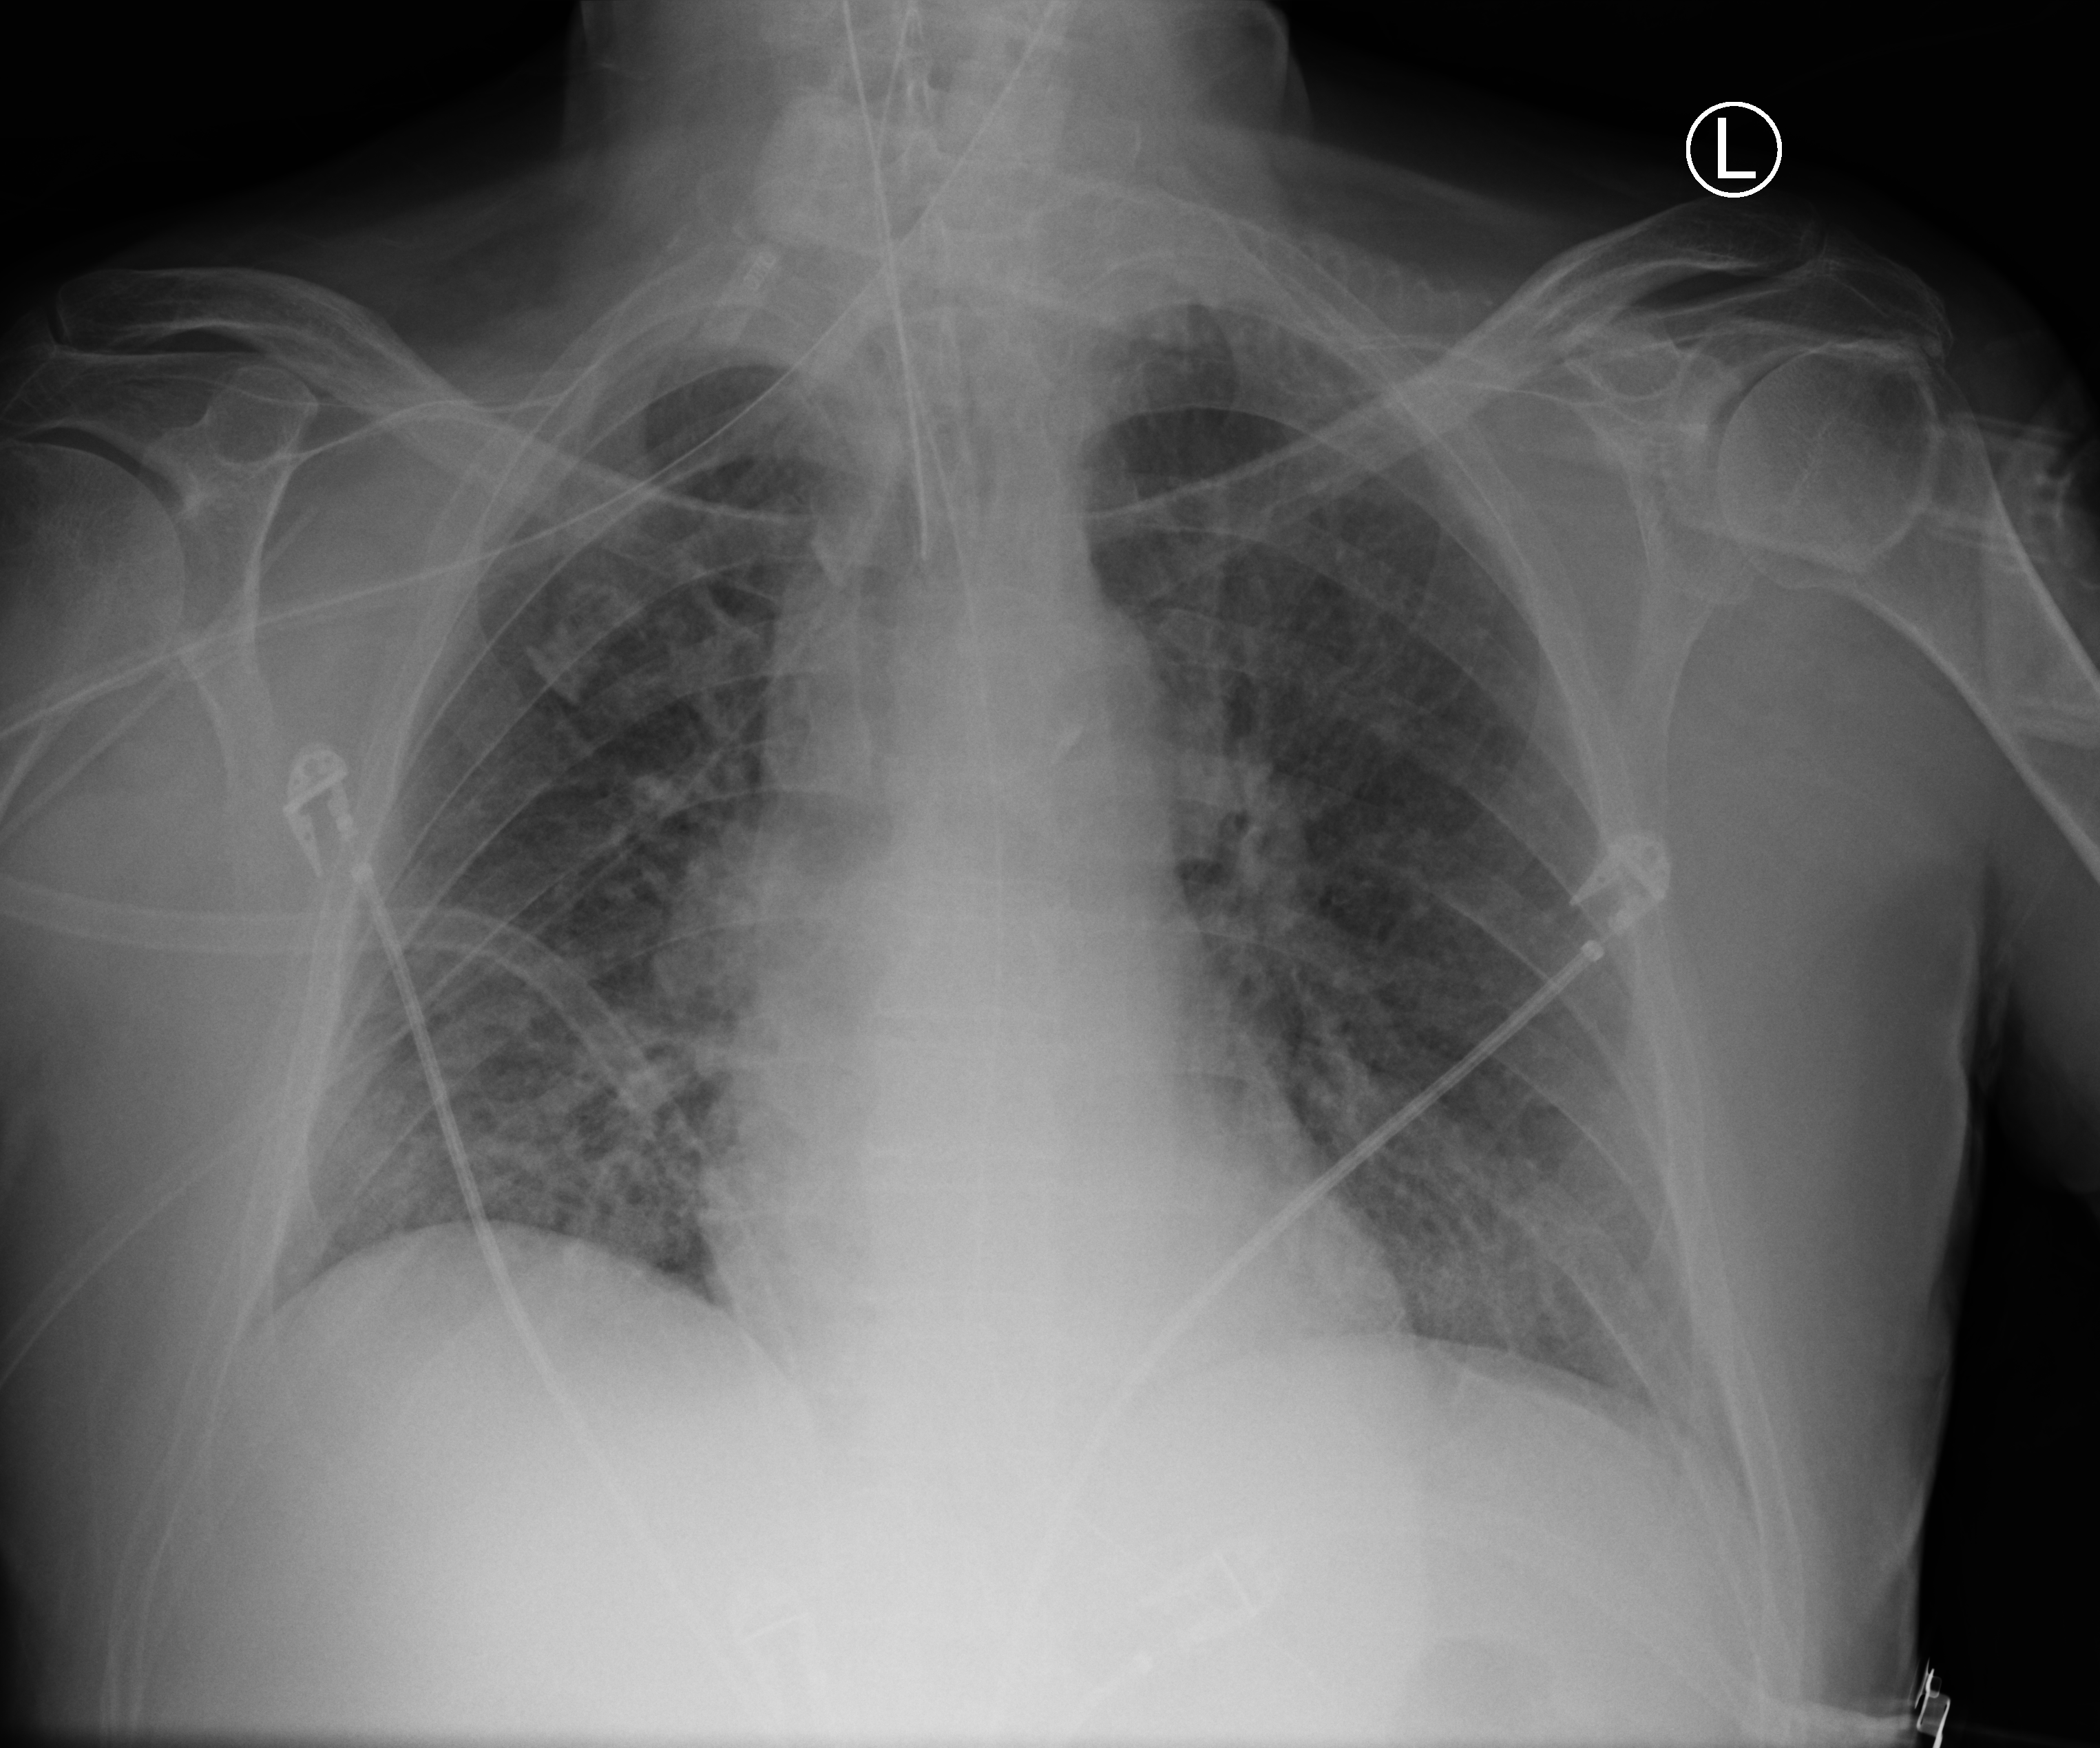
Portable chest radiograph. Male patient hospitalised with COVID-19, age 60–74 years.
From the hospital-stay record, not from the radiograph (when in the stay this image was taken is not recorded): mechanically ventilated during this hospital stay: yes; admitted to intensive care during this hospital stay: yes.